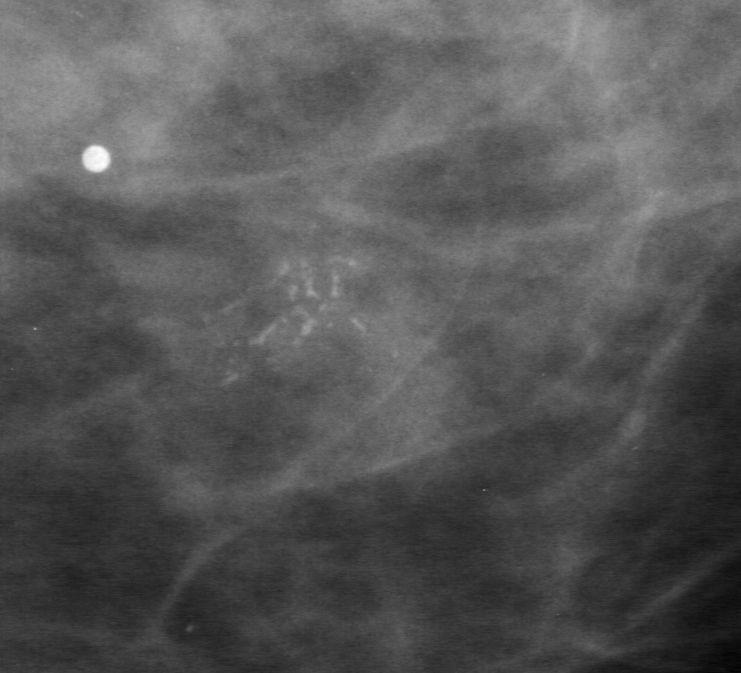
Cropped region of a digitized screen-film mammogram centred on a radiologist-marked abnormality, left breast, CC view.
Marked abnormality: calcifications, morphology fine linear branching, distribution clustered; BI-RADS assessment category 5; subtlety rating 4 on a 1 (subtle) to 5 (obvious) scale; pathology result (as recorded, not read from the image): malignant.